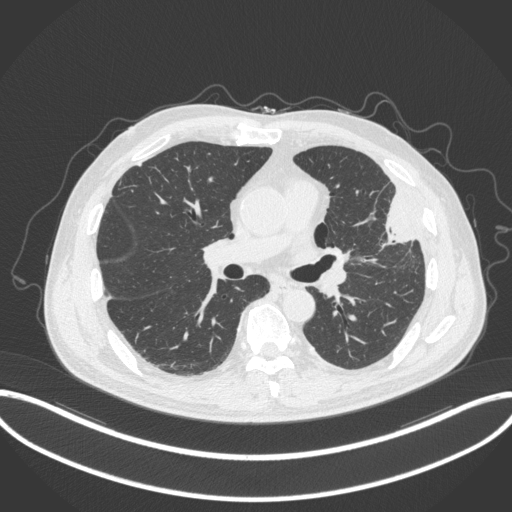
Chest CT, one axial slice; position 185 of 382 along the scan axis; reconstruction kernel B31f; 120 kVp; lung window (W 1500 / L -600 HU); 1 mm slice thickness; 512 × 512 image matrix, field of view 415 × 415 mm. Patient: male, 64 years. Case-level facts recorded for this patient, not image findings: clinical TNM (as recorded): T4 N1 M0; histopathological grade: G3.
Structures marked on this image (bounding box drawn by a radiologist):
- lung tumour (recorded histology: adenocarcinoma): bounding box [x1, y1, x2, y2] px = [369, 186, 416, 250]